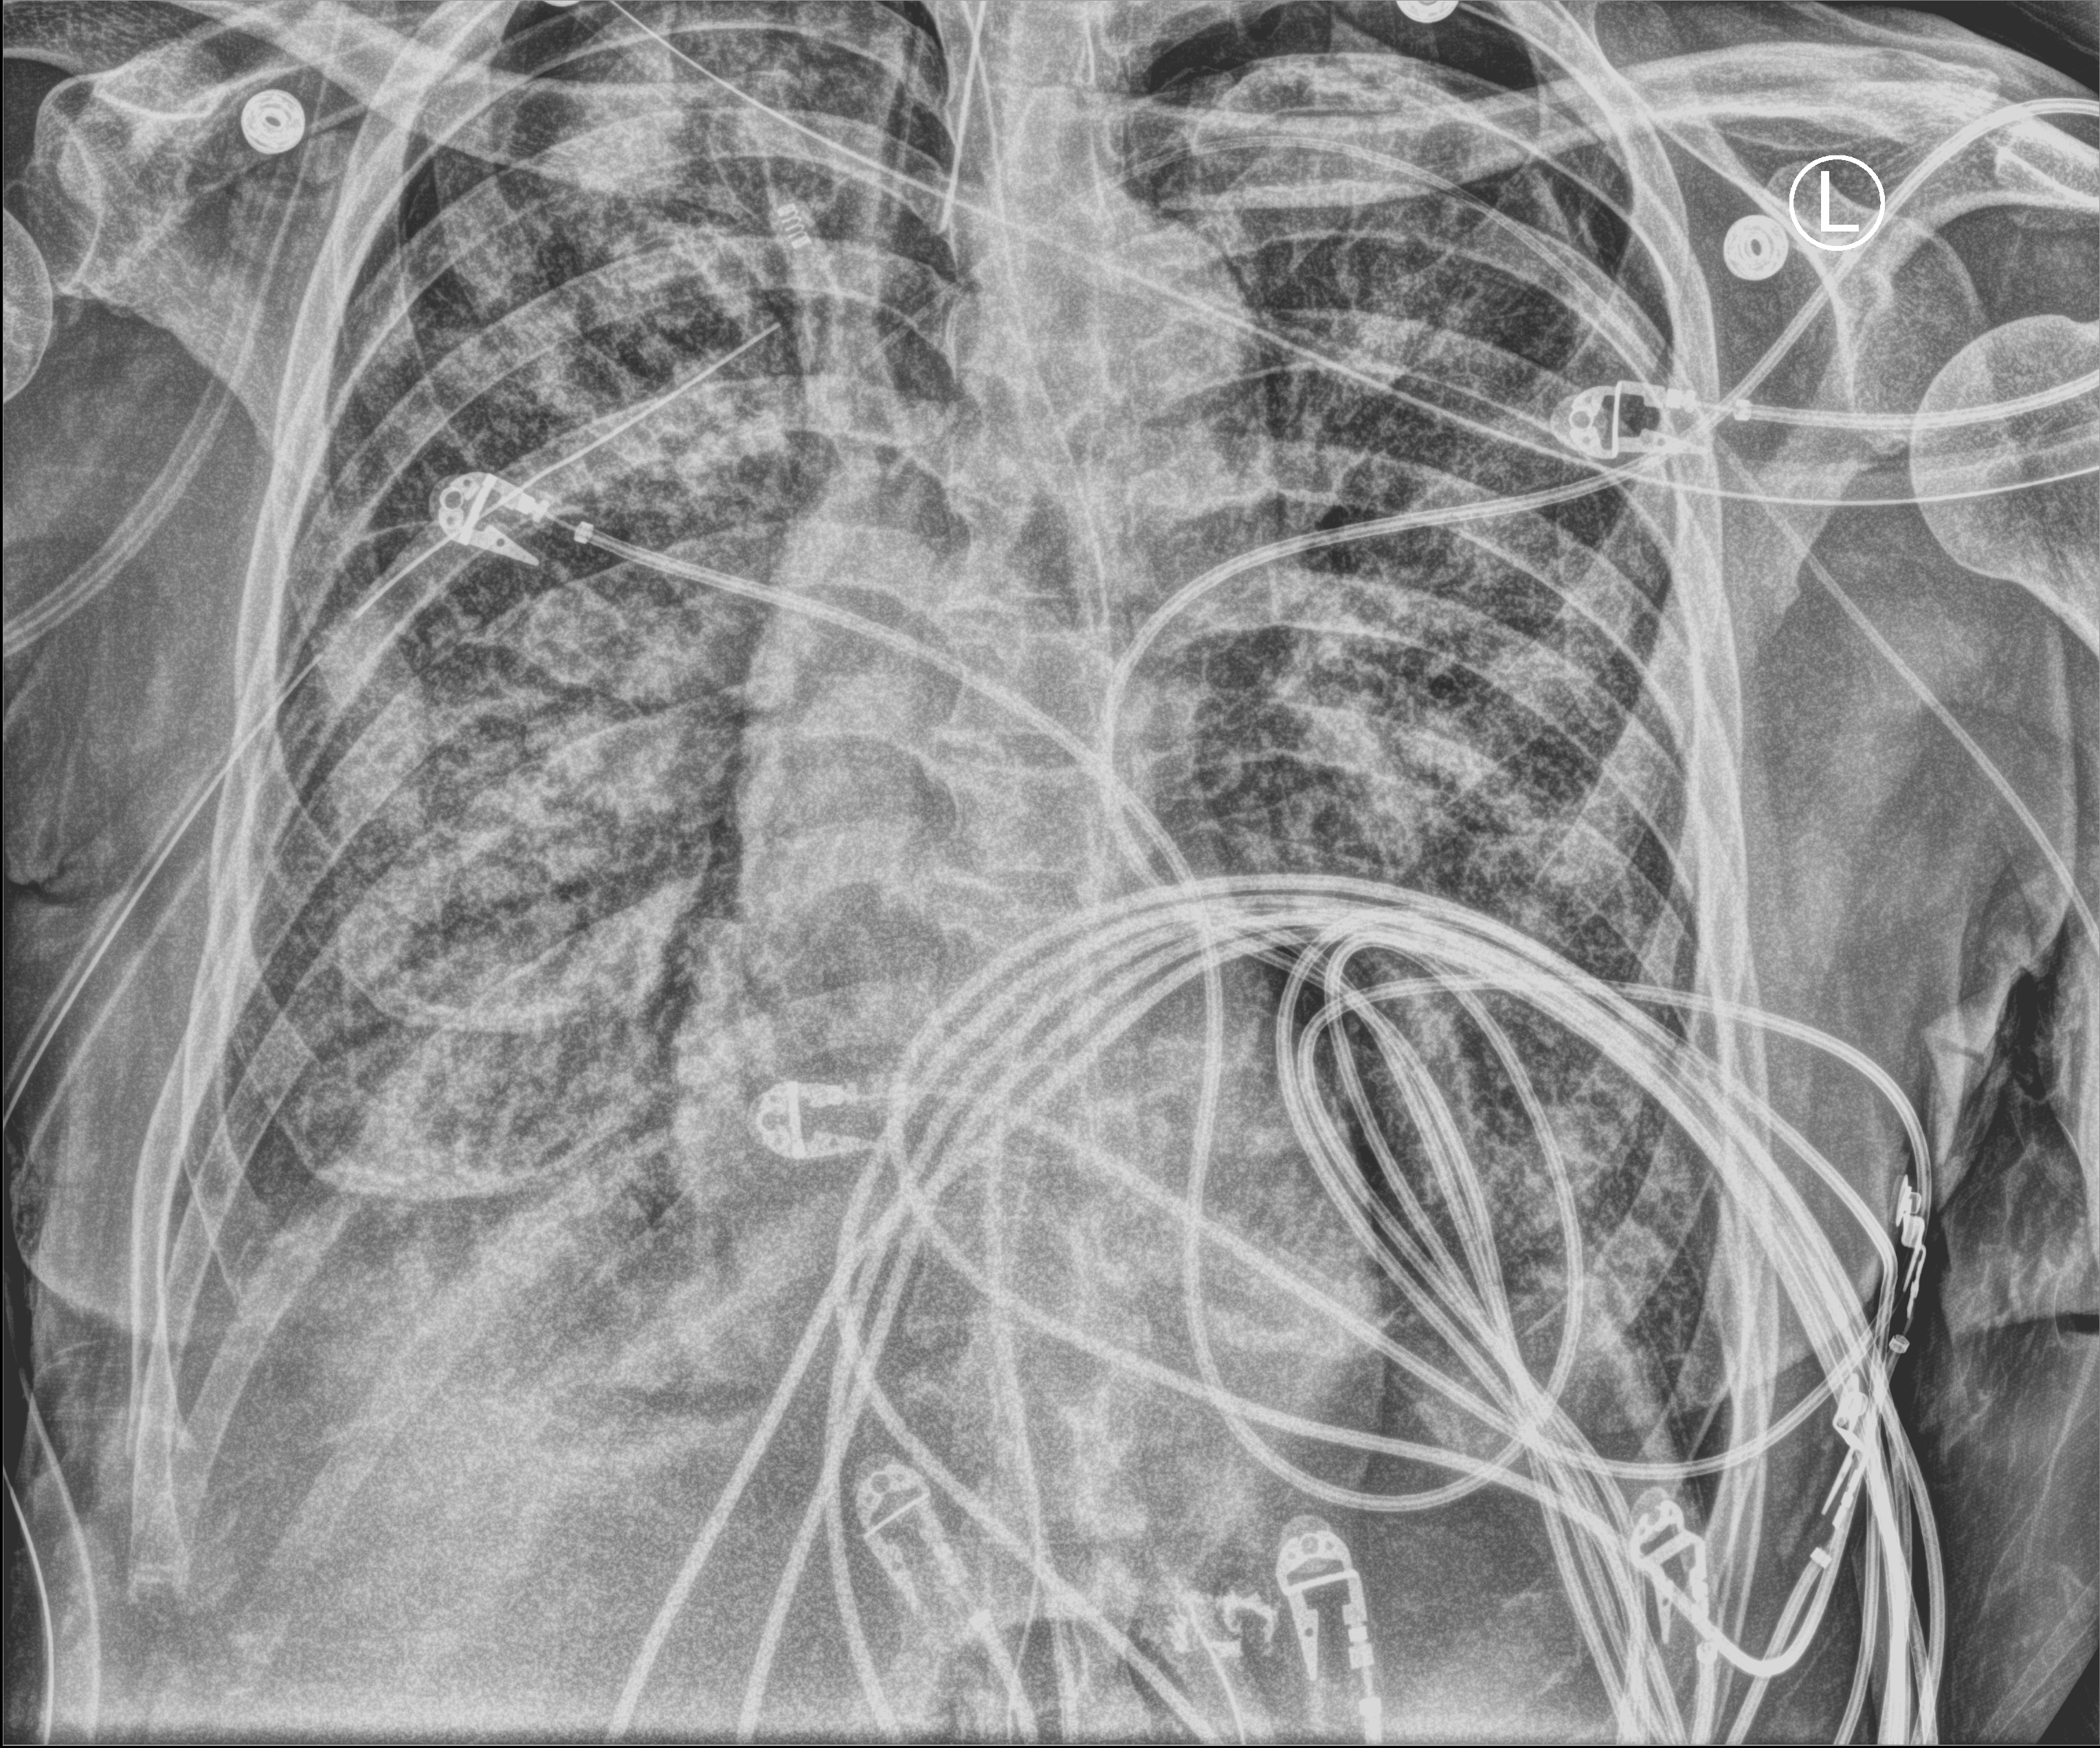
Portable chest radiograph, anteroposterior (AP) projection. Patient hospitalised with COVID-19; male, aged 60–74 years.
Admission-level facts for this patient (not findings on this image; timing relative to this image not recorded):
- length of hospital stay: 31 days
- mechanically ventilated during this hospital stay: yes